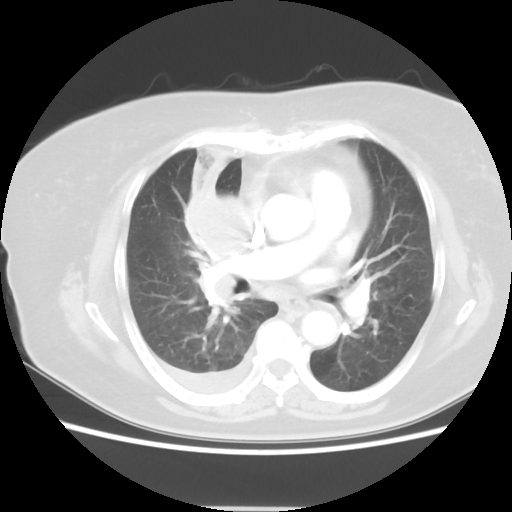
Chest CT, one axial slice; position 26 of 48 along the scan axis; reconstruction kernel STANDARD; lung window (W 1500 / L -600 HU); 5 mm slice thickness; 512 × 512 image matrix, field of view 360 × 360 mm. Female patient, age 73 years. From the clinical record (not read from this slice): clinical TNM (as recorded): T3 N3 M1b; histopathological grade: G3.
Annotated regions visible in this slice (bounding box drawn by a radiologist):
- lung tumour (recorded histology: small cell carcinoma): bounding box [x1, y1, x2, y2] px = [179, 161, 267, 309]